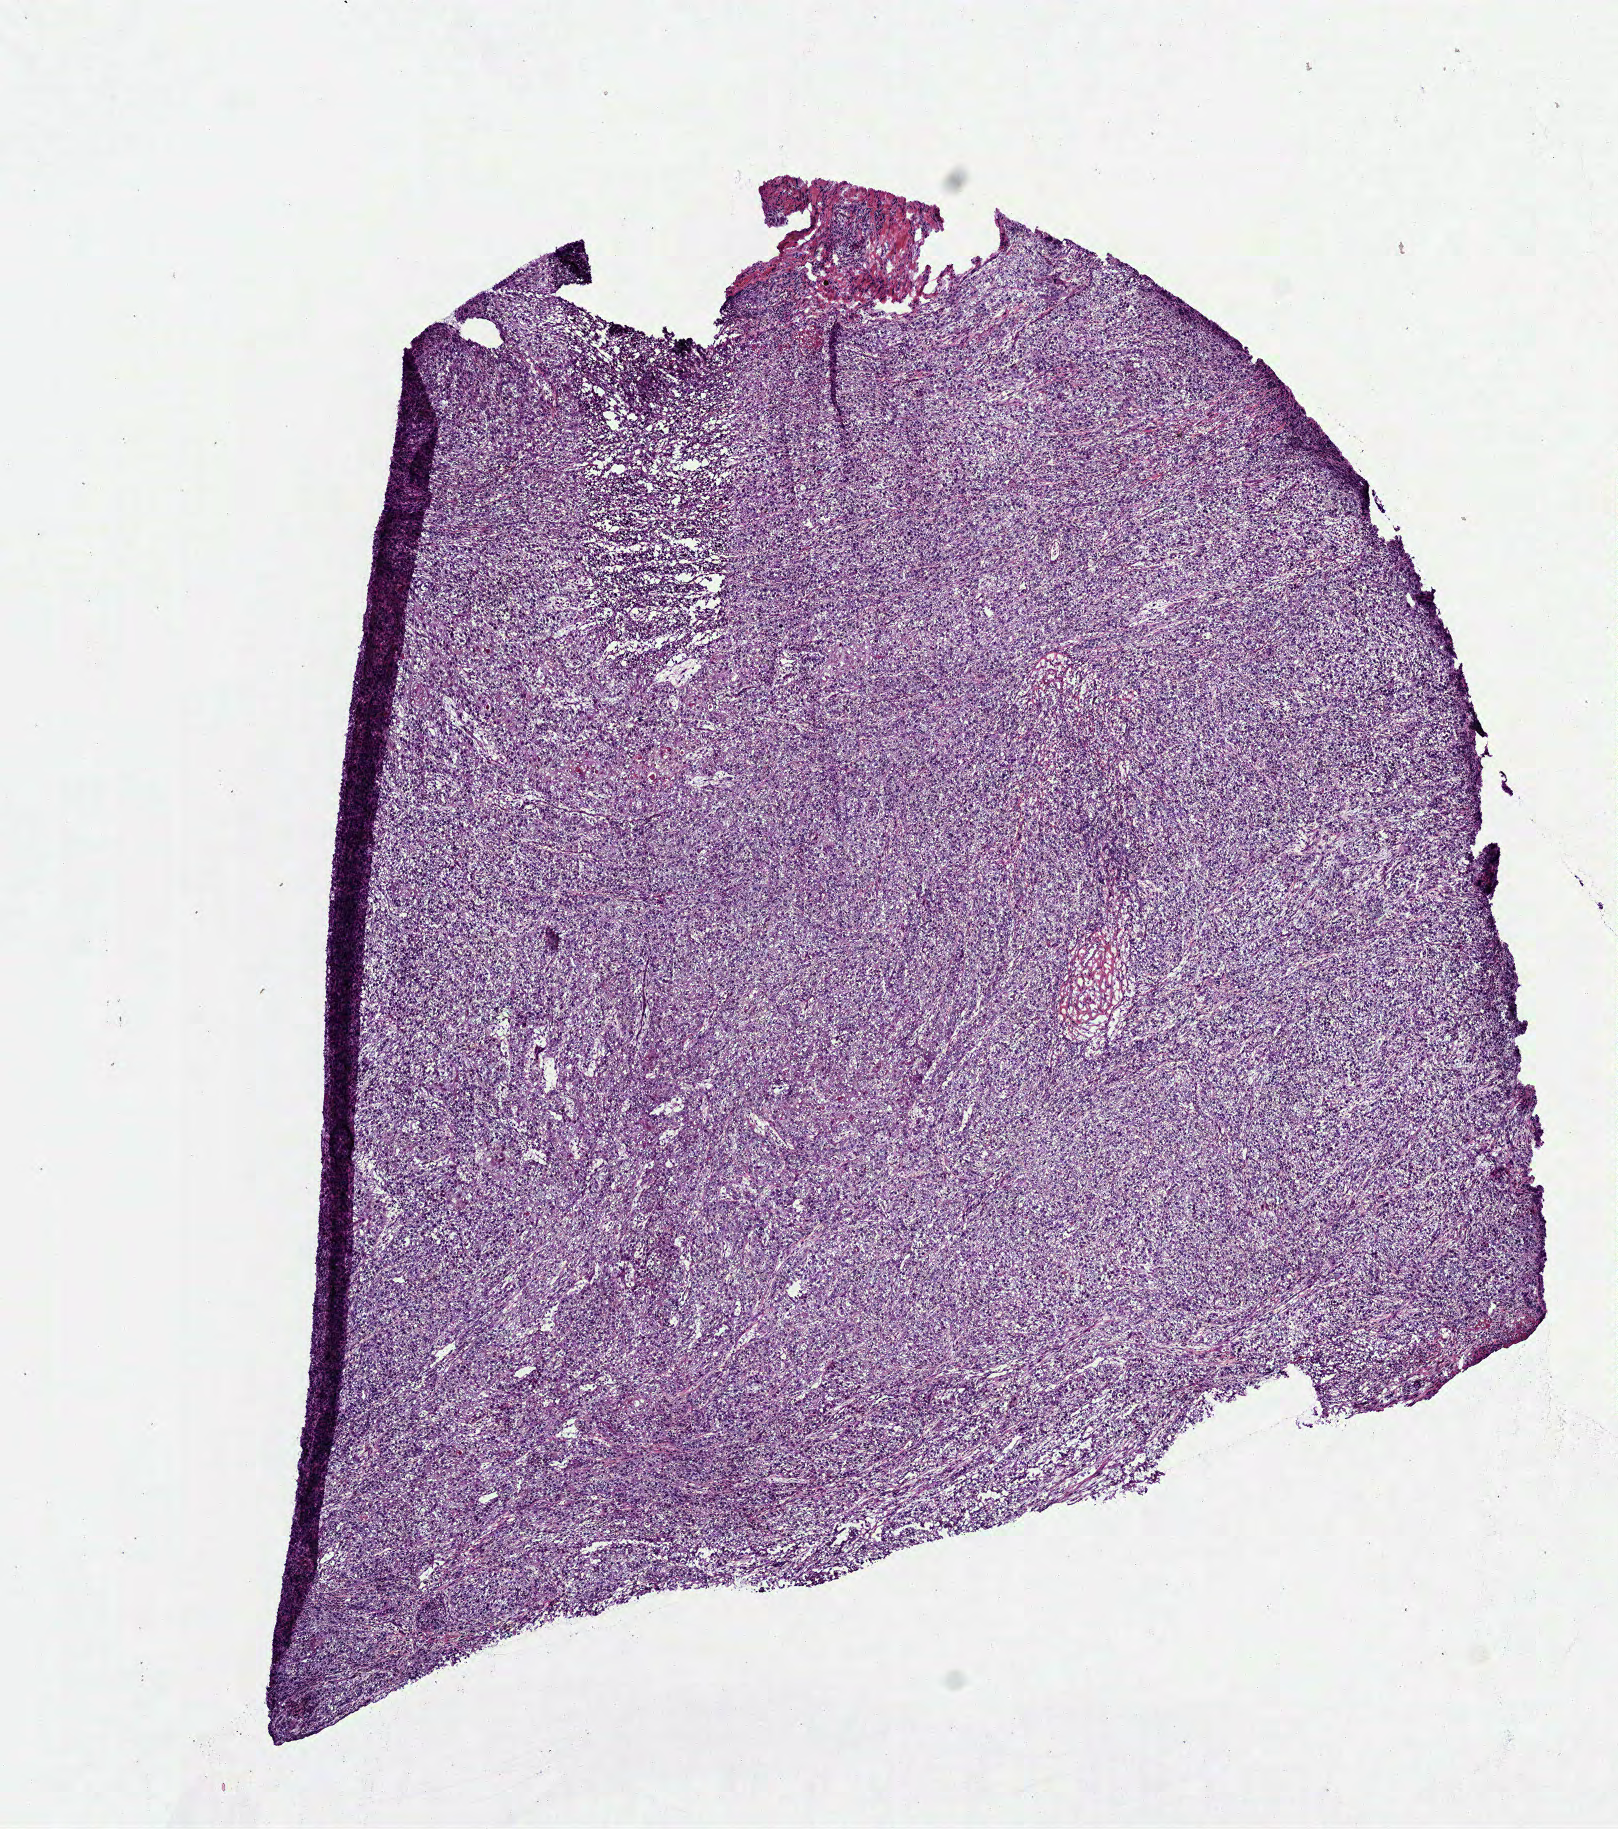
Hematoxylin and eosin (H&E) stained whole-slide image, a low-resolution overview of the entire scanned area, about 6.5 x 7.4 mm (from a 40x scan); frozen section from the bottom of the tissue portion; sample: primary tumour, head and neck. Male, age 57 years at initial diagnosis. Histologic grade: G3 (poorly differentiated). Slide review estimates, as recorded: tumour cells 95%, tumour nuclei 85%, normal cells 0%, stromal cells 5%, necrosis 0%.
AJCC pathologic stage: IVA (7th edition). Histologic diagnosis: Squamous cell carcinoma, NOS (gum, NOS). TNM: T4a N0.